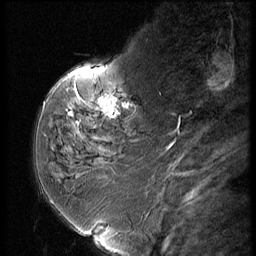
Breast MRI (dynamic contrast-enhanced), one sagittal slice; slice 16 of 56 in the series (ordered by position); dynamic contrast-enhanced series, image 2 of 3 at this slice position (ordered by acquisition); 1.5 T; TE 4.2 ms, TR 9 ms; 256 × 256 image matrix. Patient: female, 59 years. From the clinical record (not read from this slice): setting: breast cancer imaged before/during neoadjuvant chemotherapy; receptor status: HER2-positive.
Outlined on this slice (semi-automatic segmentation, software-assisted and operator-edited):
- analysis volume of interest (the breast-tissue region the enhancement analysis was run in; not a lesion): box from (x=44, y=66) to (x=151, y=135) px
- tumour enhancement mask (voxels above the 140 % enhancement threshold inside the analysis volume of interest): (x=69, y=98)–(x=119, y=117)